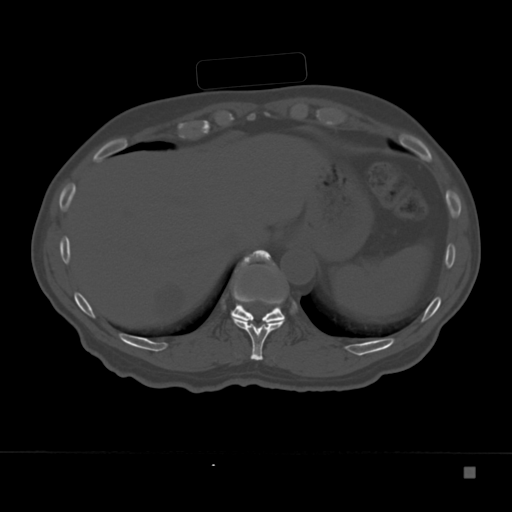
CT including the spine, one axial slice; slice 163 of 332 in the series (ordered by position); reconstruction kernel Br40s; 120 kVp; bone window (W 1800 / L 400 HU); 1.5 mm slice thickness; 512 × 512 image matrix. Patient: male, 72 years. From the clinical record (not read from this slice): primary cancer: skeletal.
Structures marked on this image (semi-automatically segmented with operator editing):
- T10 vertebra: bounding box (x1, y1, x2, y2) in pixels: (231, 251, 283, 360)
- T11 vertebra: (231, 250, 285, 323)